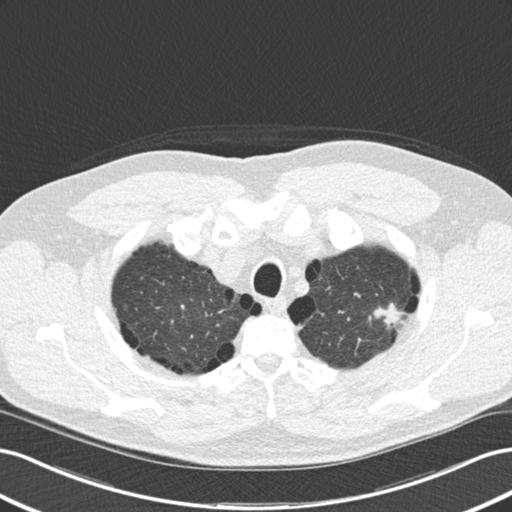
Low-dose screening chest CT, one axial slice; slice 143 of 177 in the series (ordered by position); reconstruction kernel B30f; lung window (W 1500 / L -600 HU); 512 × 512 image matrix, field of view 360 × 360 mm.
Outlined on this slice (outlined manually by an expert reader):
- lesion 1 (tumor, upper lobe of left lung): bounding box (x1, y1, x2, y2) in pixels: (373, 303, 404, 328)